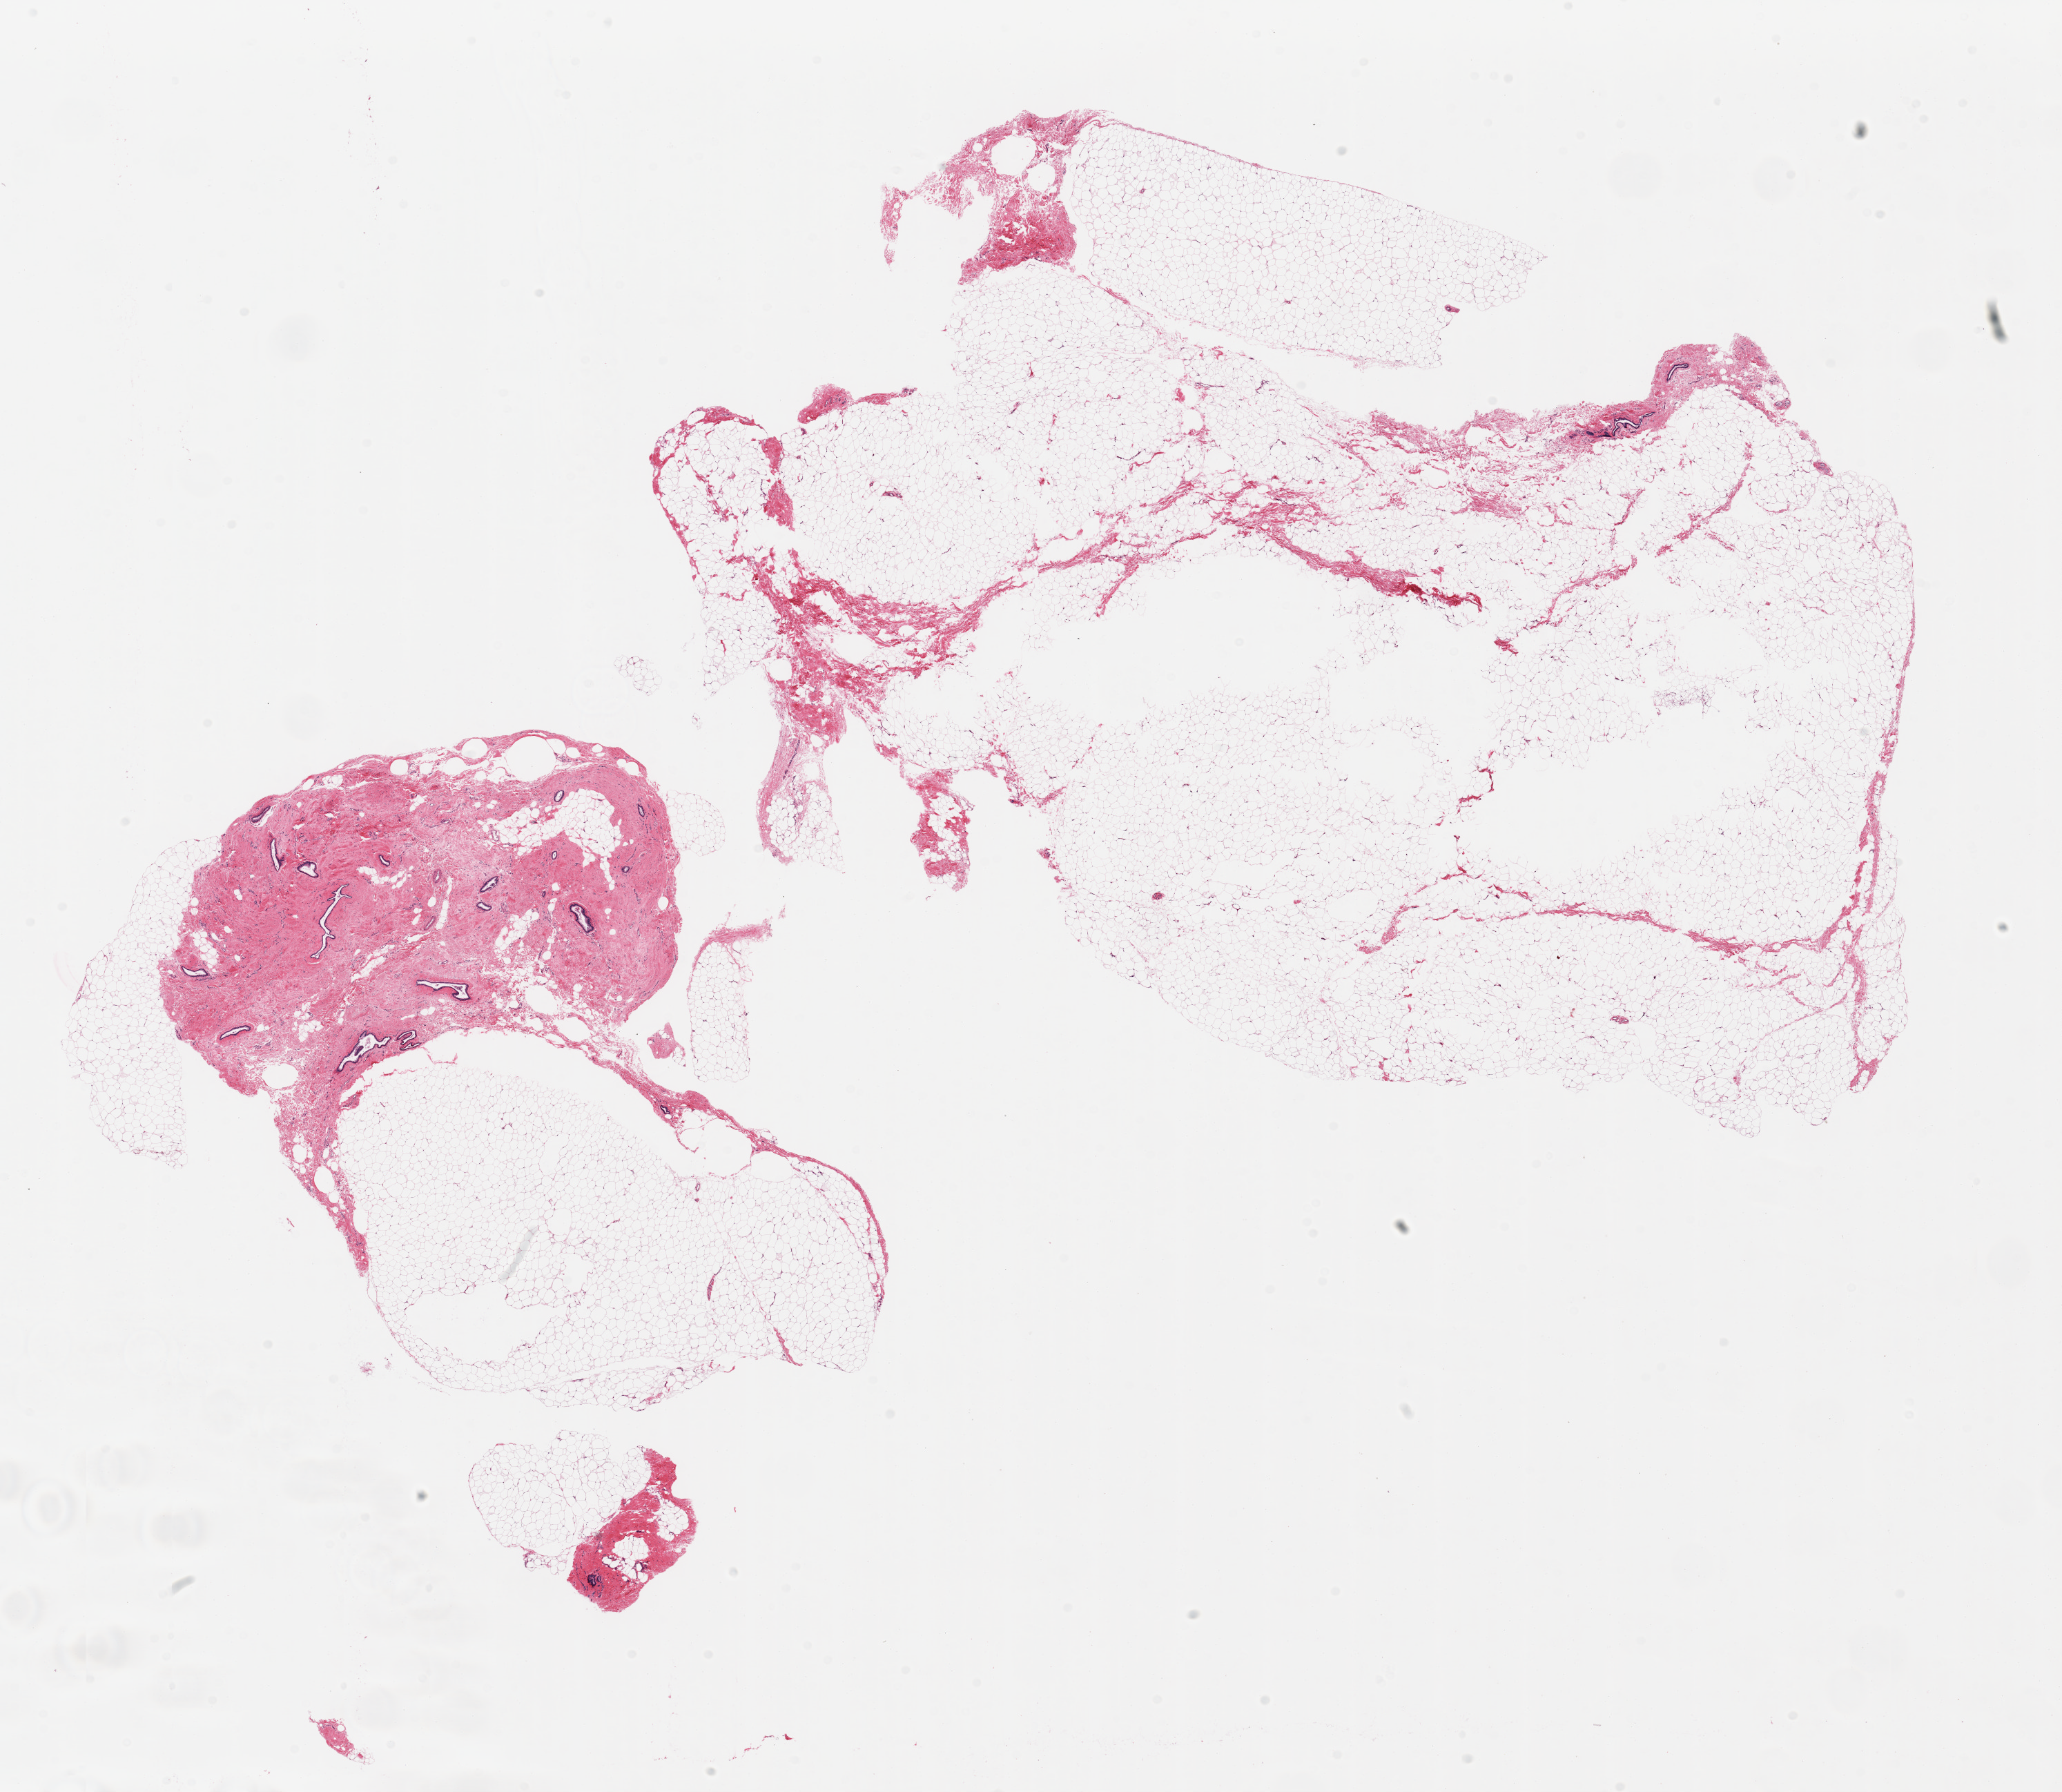
Digitized H&E-stained section, shown as a low-resolution overview of the whole scanned area (about 23.6 x 20.5 mm, acquisition: 20x scan); PAXgene-fixed paraffin-embedded (PFPE) section; target tissue: breast; tissue donor sample.
Review note (as recorded): 2 pieces, localized stromal and ductal gynecomastoid hyperplasia.